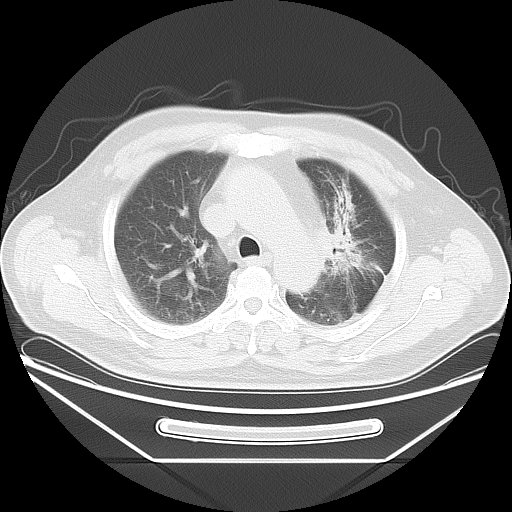
Chest CT, one axial slice; position 28 of 37 along the scan axis; reconstruction kernel LUNG; 120 kVp; lung window (W 1500 / L -600 HU); 5 mm slice thickness; 512 × 512 image matrix, field of view 411 × 411 mm. Patient: male, 61 years. From the clinical record (not read from this slice): clinical TNM (as recorded): T2a N0 M0.
Outlined on this slice (rectangle marked by the reading radiologist):
- lung tumour (recorded histology: small cell carcinoma): box from (x=321, y=170) to (x=398, y=298) px